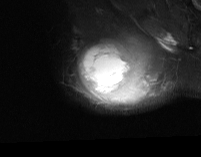
MRI of an extremity soft-tissue mass, one axial slice; slice 55 of 74 in the series (ordered by position); STIR; MR volume resampled by the dataset authors to the PET/CT grid (not the native acquisition matrix); 201 × 157 image matrix, field of view 196 × 153 mm. Male patient. Case-level facts recorded for this patient, not image findings: histological type: pleiomorphic spindle cell undifferentiated; grade: high; site of the primary tumour: right parascapusular.
Annotated regions visible in this slice (expert contour drawn on MRI and transferred to this co-registered scan by the dataset authors):
- gross tumour volume including surrounding oedema: bounding box <76,36,173,106> (left, top, right, bottom; pixels)
- gross tumour volume (mass): <79,43,145,103>